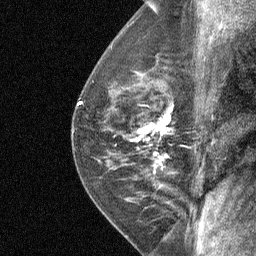
Breast MRI (dynamic contrast-enhanced), one sagittal slice; position 41 of 64 along the scan axis; dynamic contrast-enhanced study with each time point stored as its own series, time point 2 of 4 at this slice position (early post-contrast, ordered by acquisition time); 1.5 T; TE 4.8 ms, TR 27 ms; 256 × 256 image matrix, field of view 180 × 180 mm. Patient: female, 50 years. From the clinical record (not read from this slice): setting: breast cancer imaged before/during neoadjuvant chemotherapy; receptor status: HER2-positive.
Structures marked on this image (semi-automatic segmentation, software-assisted and operator-edited):
- analysis volume of interest (the breast-tissue region the enhancement analysis was run in; not a lesion): bounding box <123,91,176,177> (left, top, right, bottom; pixels)
- tumour enhancement mask (voxels above the 90 % enhancement threshold inside the analysis volume of interest): <137,105,173,161>